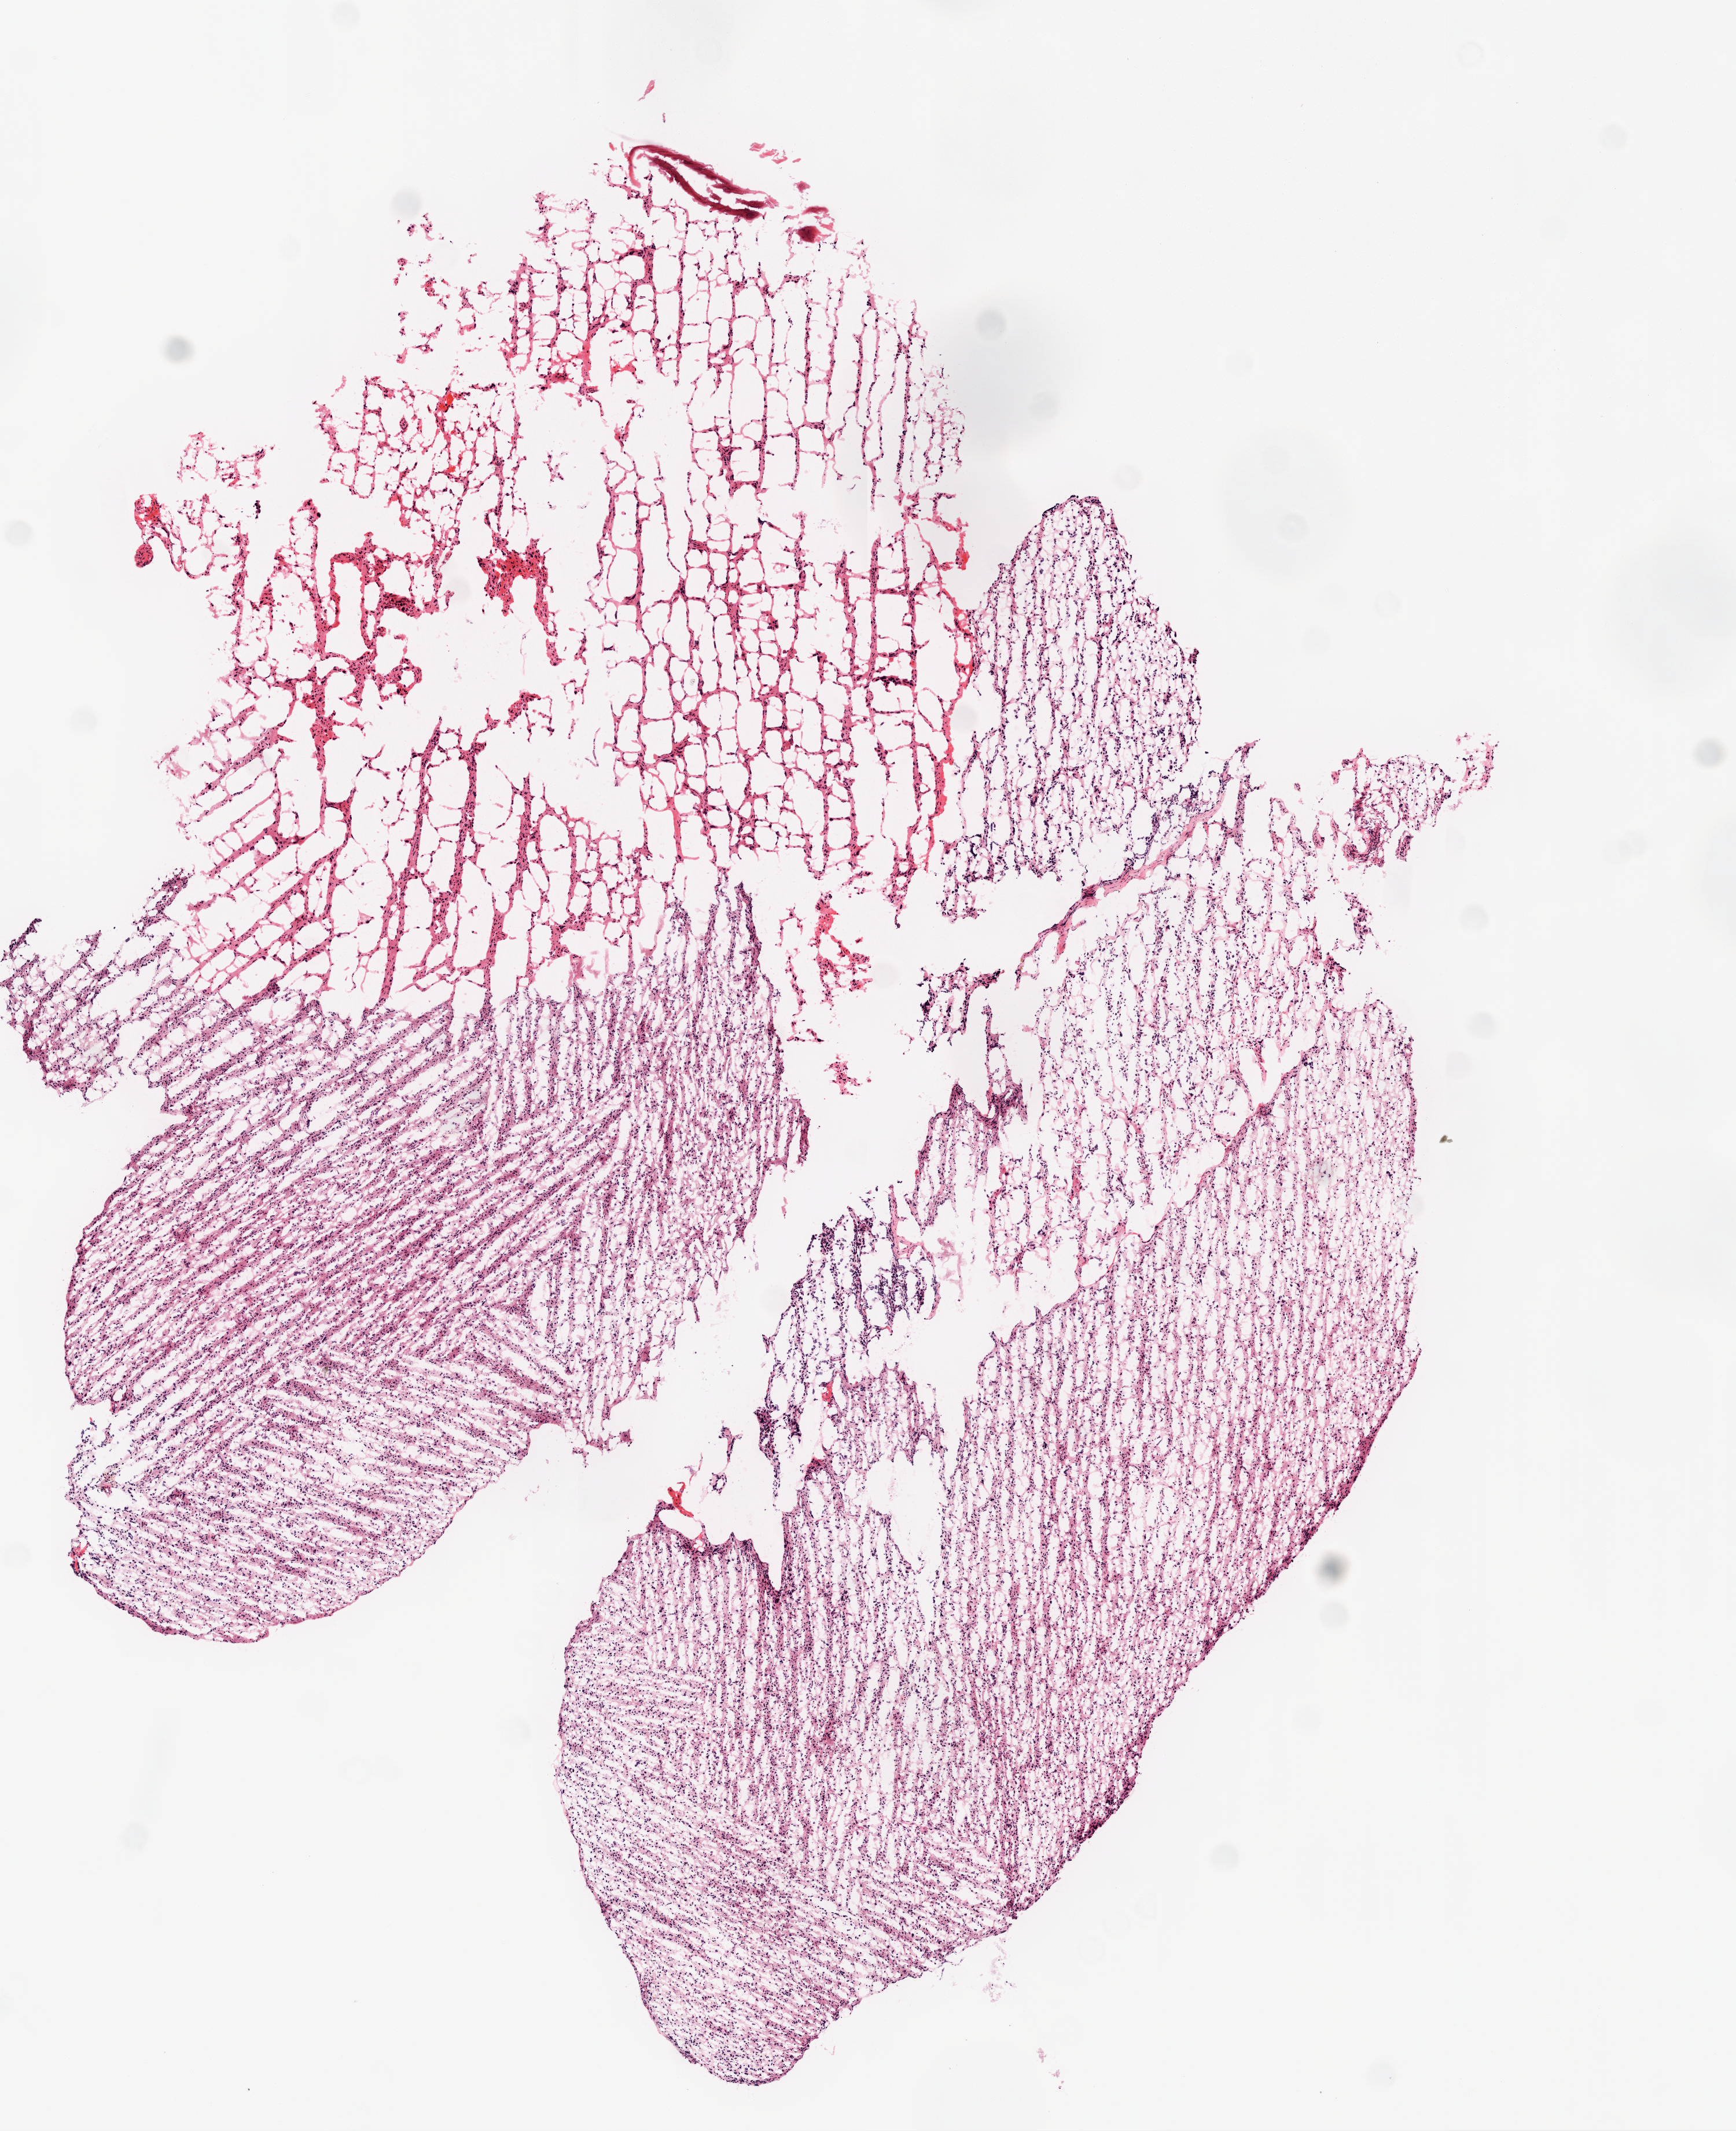
Hematoxylin and eosin (H&E) stained whole-slide image — shown as a low-resolution overview of the whole scanned area (about 6.0 x 7.4 mm, slide scanned at 20x). Frozen section from the top of the tissue portion. Brain, primary tumour sample. Male, age 58 years at initial diagnosis. Composition of this section per pathologist review: tumour cells 100%, tumour nuclei 100%, normal cells 0%, stromal cells 0%, necrosis 0%.
Histologic diagnosis: Glioblastoma.